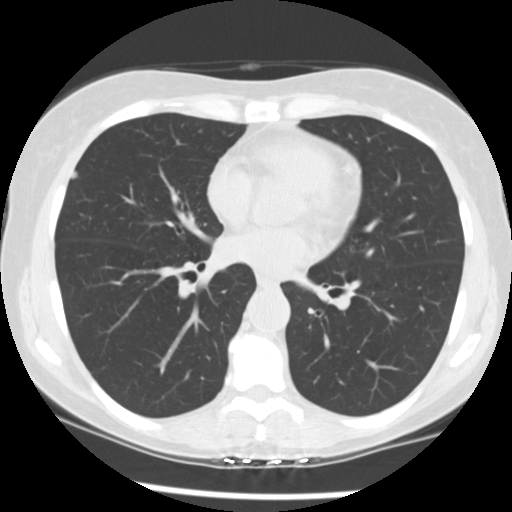
Low-dose screening chest CT, one axial slice; position 127 of 241 along the scan axis; reconstruction kernel STANDARD; 120 kVp; lung window (W 1500 / L -600 HU); 2.5 mm slice thickness; 512 × 512 image matrix, field of view 320 × 320 mm.
Structures marked on this image (expert manual segmentation):
- lesion 1 (tumor, upper lobe of right lung): box from (x=70, y=170) to (x=78, y=180) px